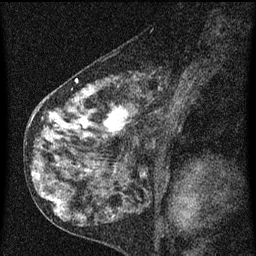
Breast MRI (dynamic contrast-enhanced), one sagittal slice; slice 32 of 60 in the series (ordered by position); dynamic contrast-enhanced series, image 2 of 3 at this slice position (ordered by acquisition); 1.5 T; TE 4.2 ms, TR 8 ms; 2 mm slice thickness; 256 × 256 image matrix. Patient: female, 55 years.
Structures marked on this image (semi-automatic segmentation, software-assisted and operator-edited):
- analysis volume of interest (the breast-tissue region the enhancement analysis was run in; not a lesion): bounding box [x1, y1, x2, y2] px = [42, 72, 185, 155]
- tumour enhancement mask (voxels above the 70 % enhancement threshold inside the analysis volume of interest): [49, 80, 133, 137]